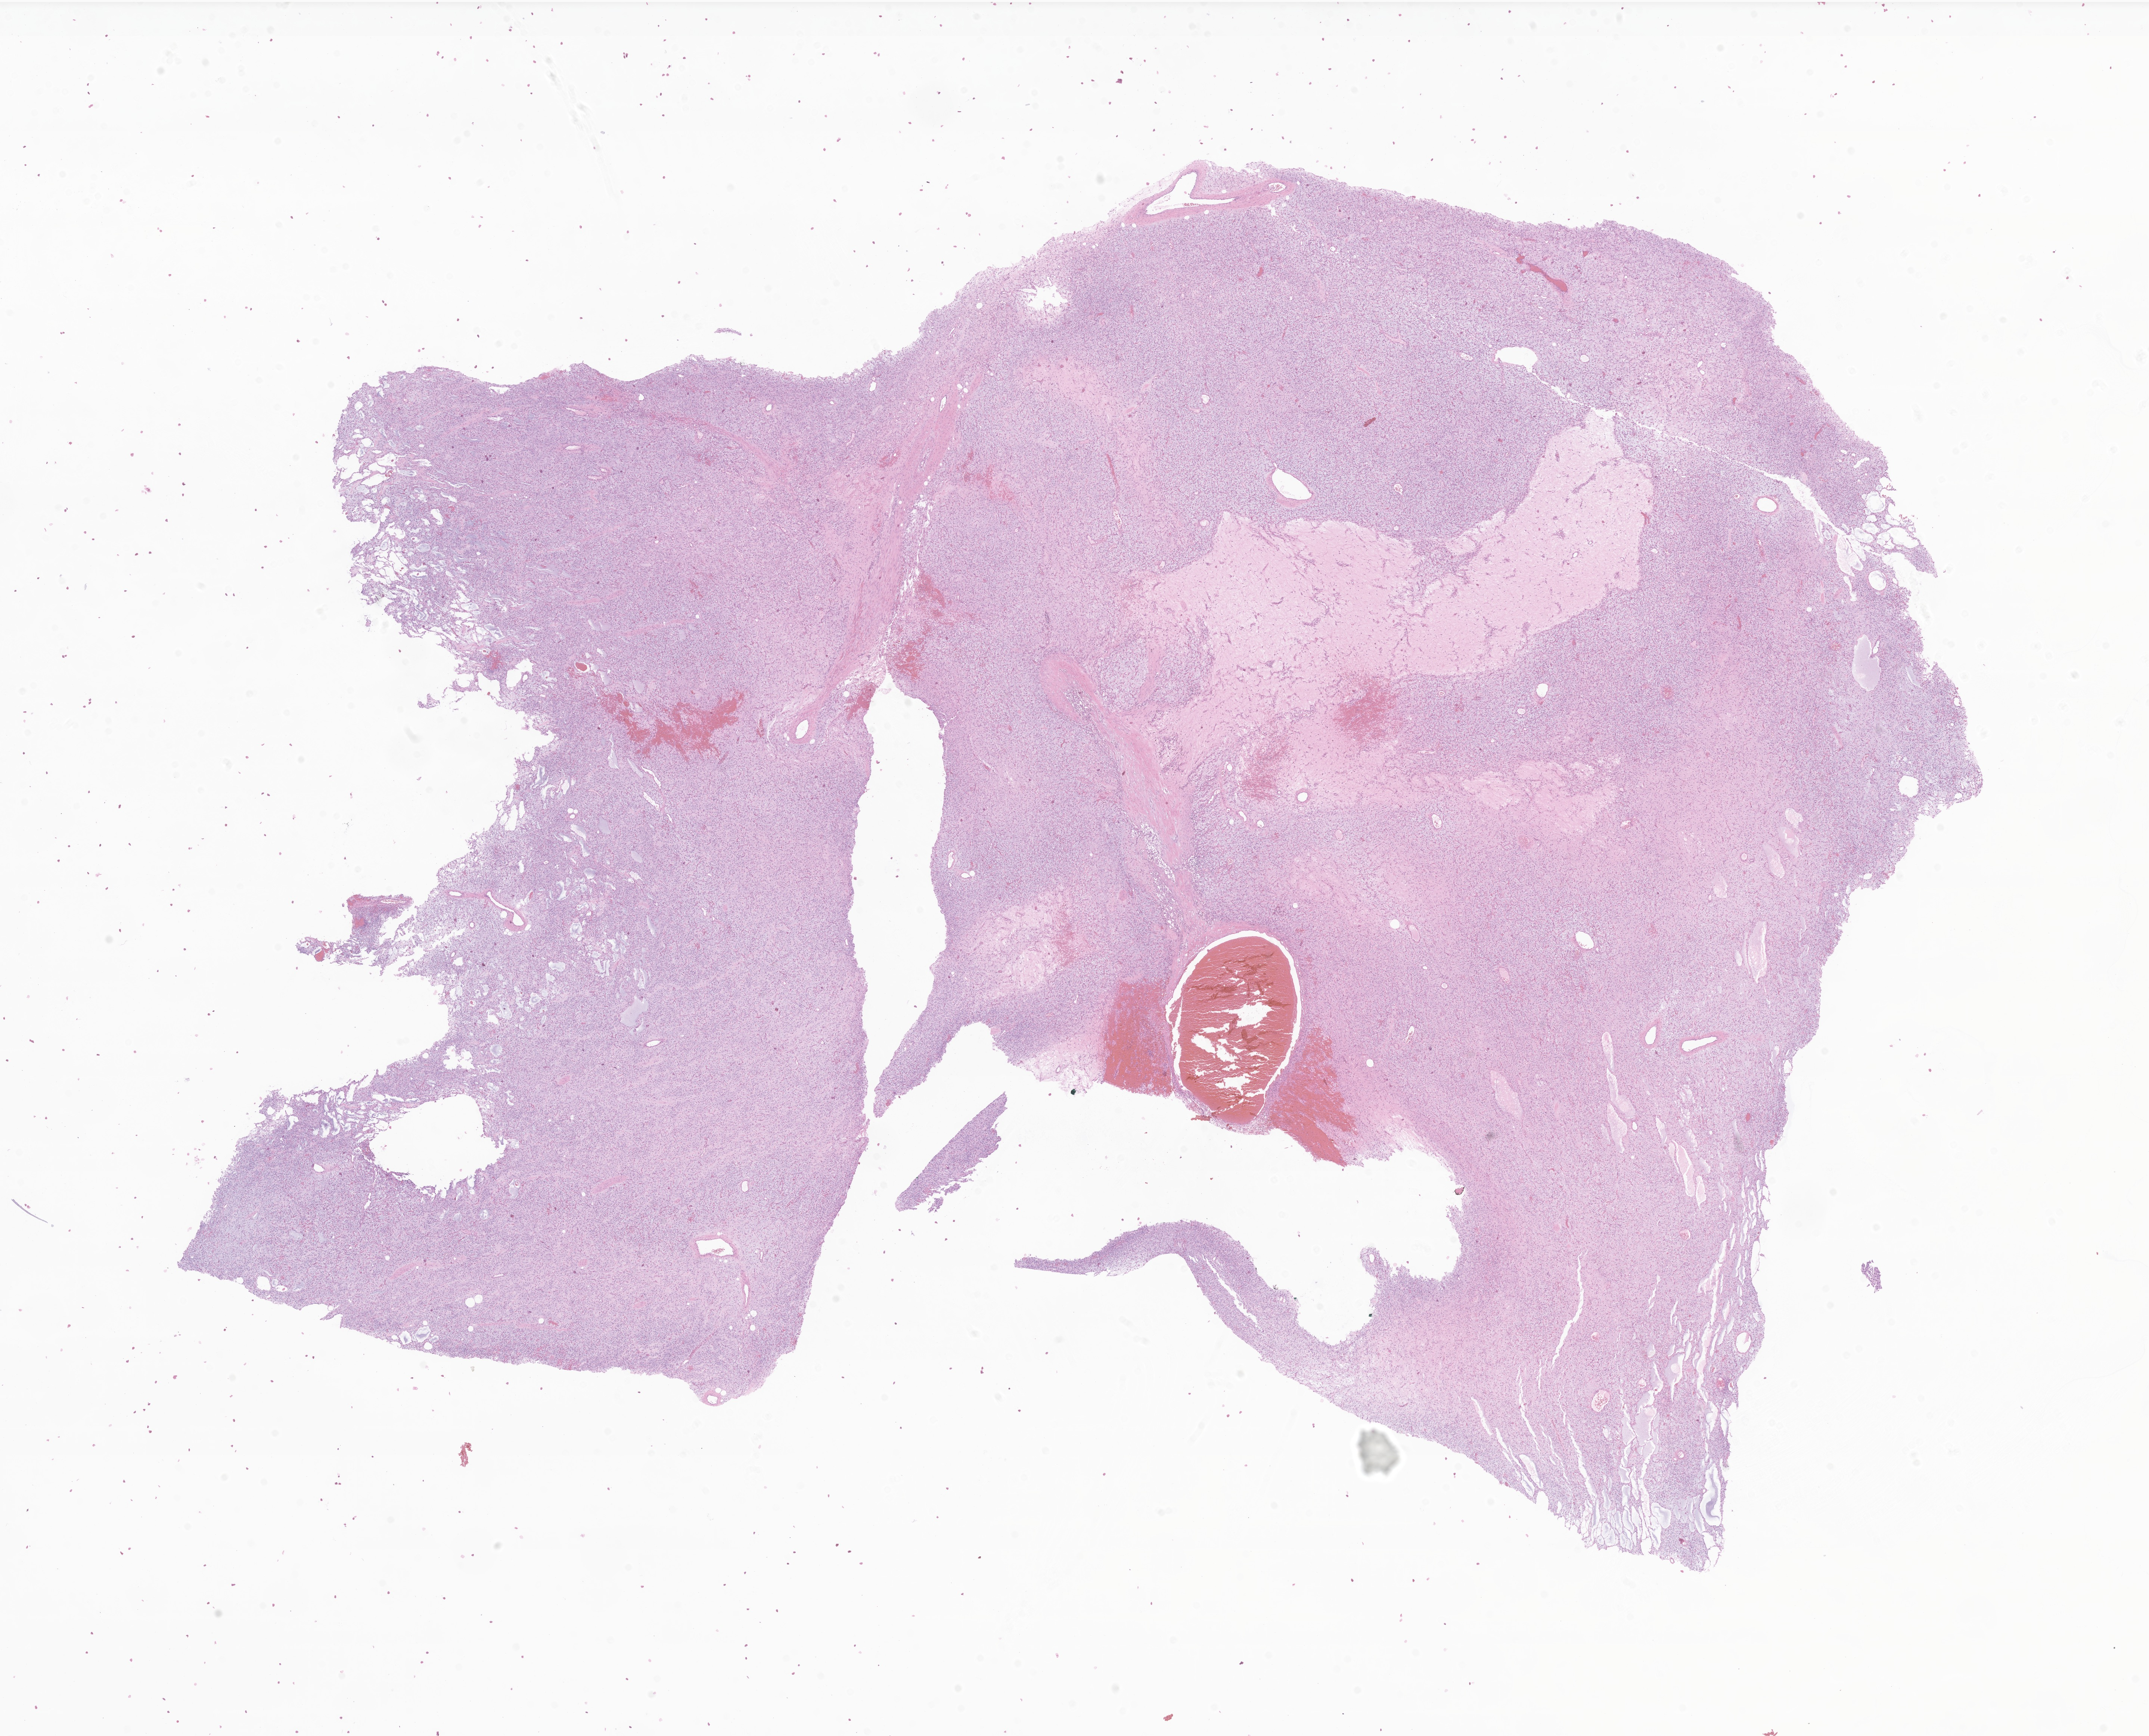
Whole-slide image, haematoxylin and eosin stain of tumor tissue from the soft tissue — shown as a low-resolution overview of the whole scanned area (about 24.3 x 19.6 mm), formalin-fixed paraffin-embedded section. Male patient, age 176 months (14 years 8 months).
Recorded diagnosis: Liposarcoma, NOS.